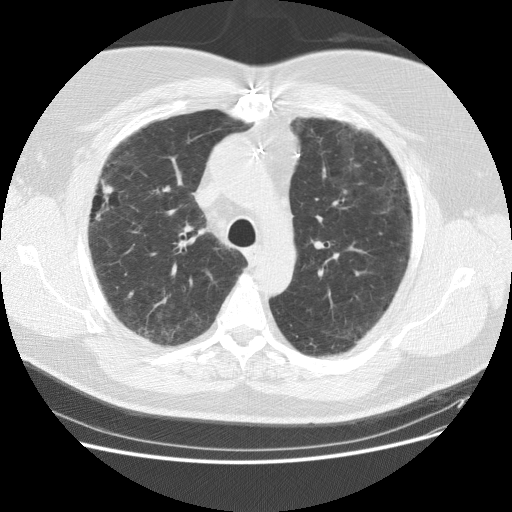
Low-dose screening chest CT, one axial slice. Position 113 of 151 along the scan axis. Reconstruction kernel STANDARD. 120 kVp. Lung window (W 1500 / L -600 HU). 2.5 mm slice thickness. 512 × 512 image matrix, field of view 378 × 378 mm.
Annotated regions visible in this slice (outlined manually by an expert reader):
- lesion 2 (tumor, upper lobe of right lung): bounding box <98,181,115,198> (left, top, right, bottom; pixels)